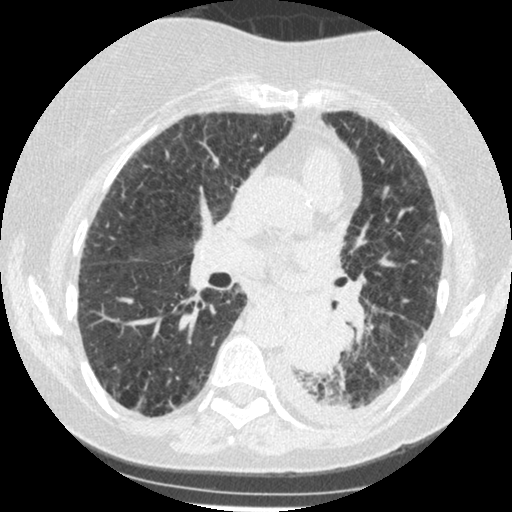
Chest CT (low-dose screening protocol), one axial image, third screening round (two years after baseline), lung window (W 1500 / L -600 HU), 1.25 mm slice thickness, slice 209 of 341 in the series, 512 × 512 image matrix, field of view 310 × 310 mm. Female participant, aged 60 years at enrolment. Former smoker at enrolment.
Lesion marked by an expert reader, bounding box <272,306,342,374> (left, top, right, bottom; pixels). Reader record for this screening exam (exam-level; its link to the box is not recorded): non-calcified nodule or mass ≥4 mm, left lower lobe, 54 × 38 mm, smooth margins, soft tissue attenuation, pre-existing on the prior screen: yes; interval growth: yes. Official screen result: positive, other.